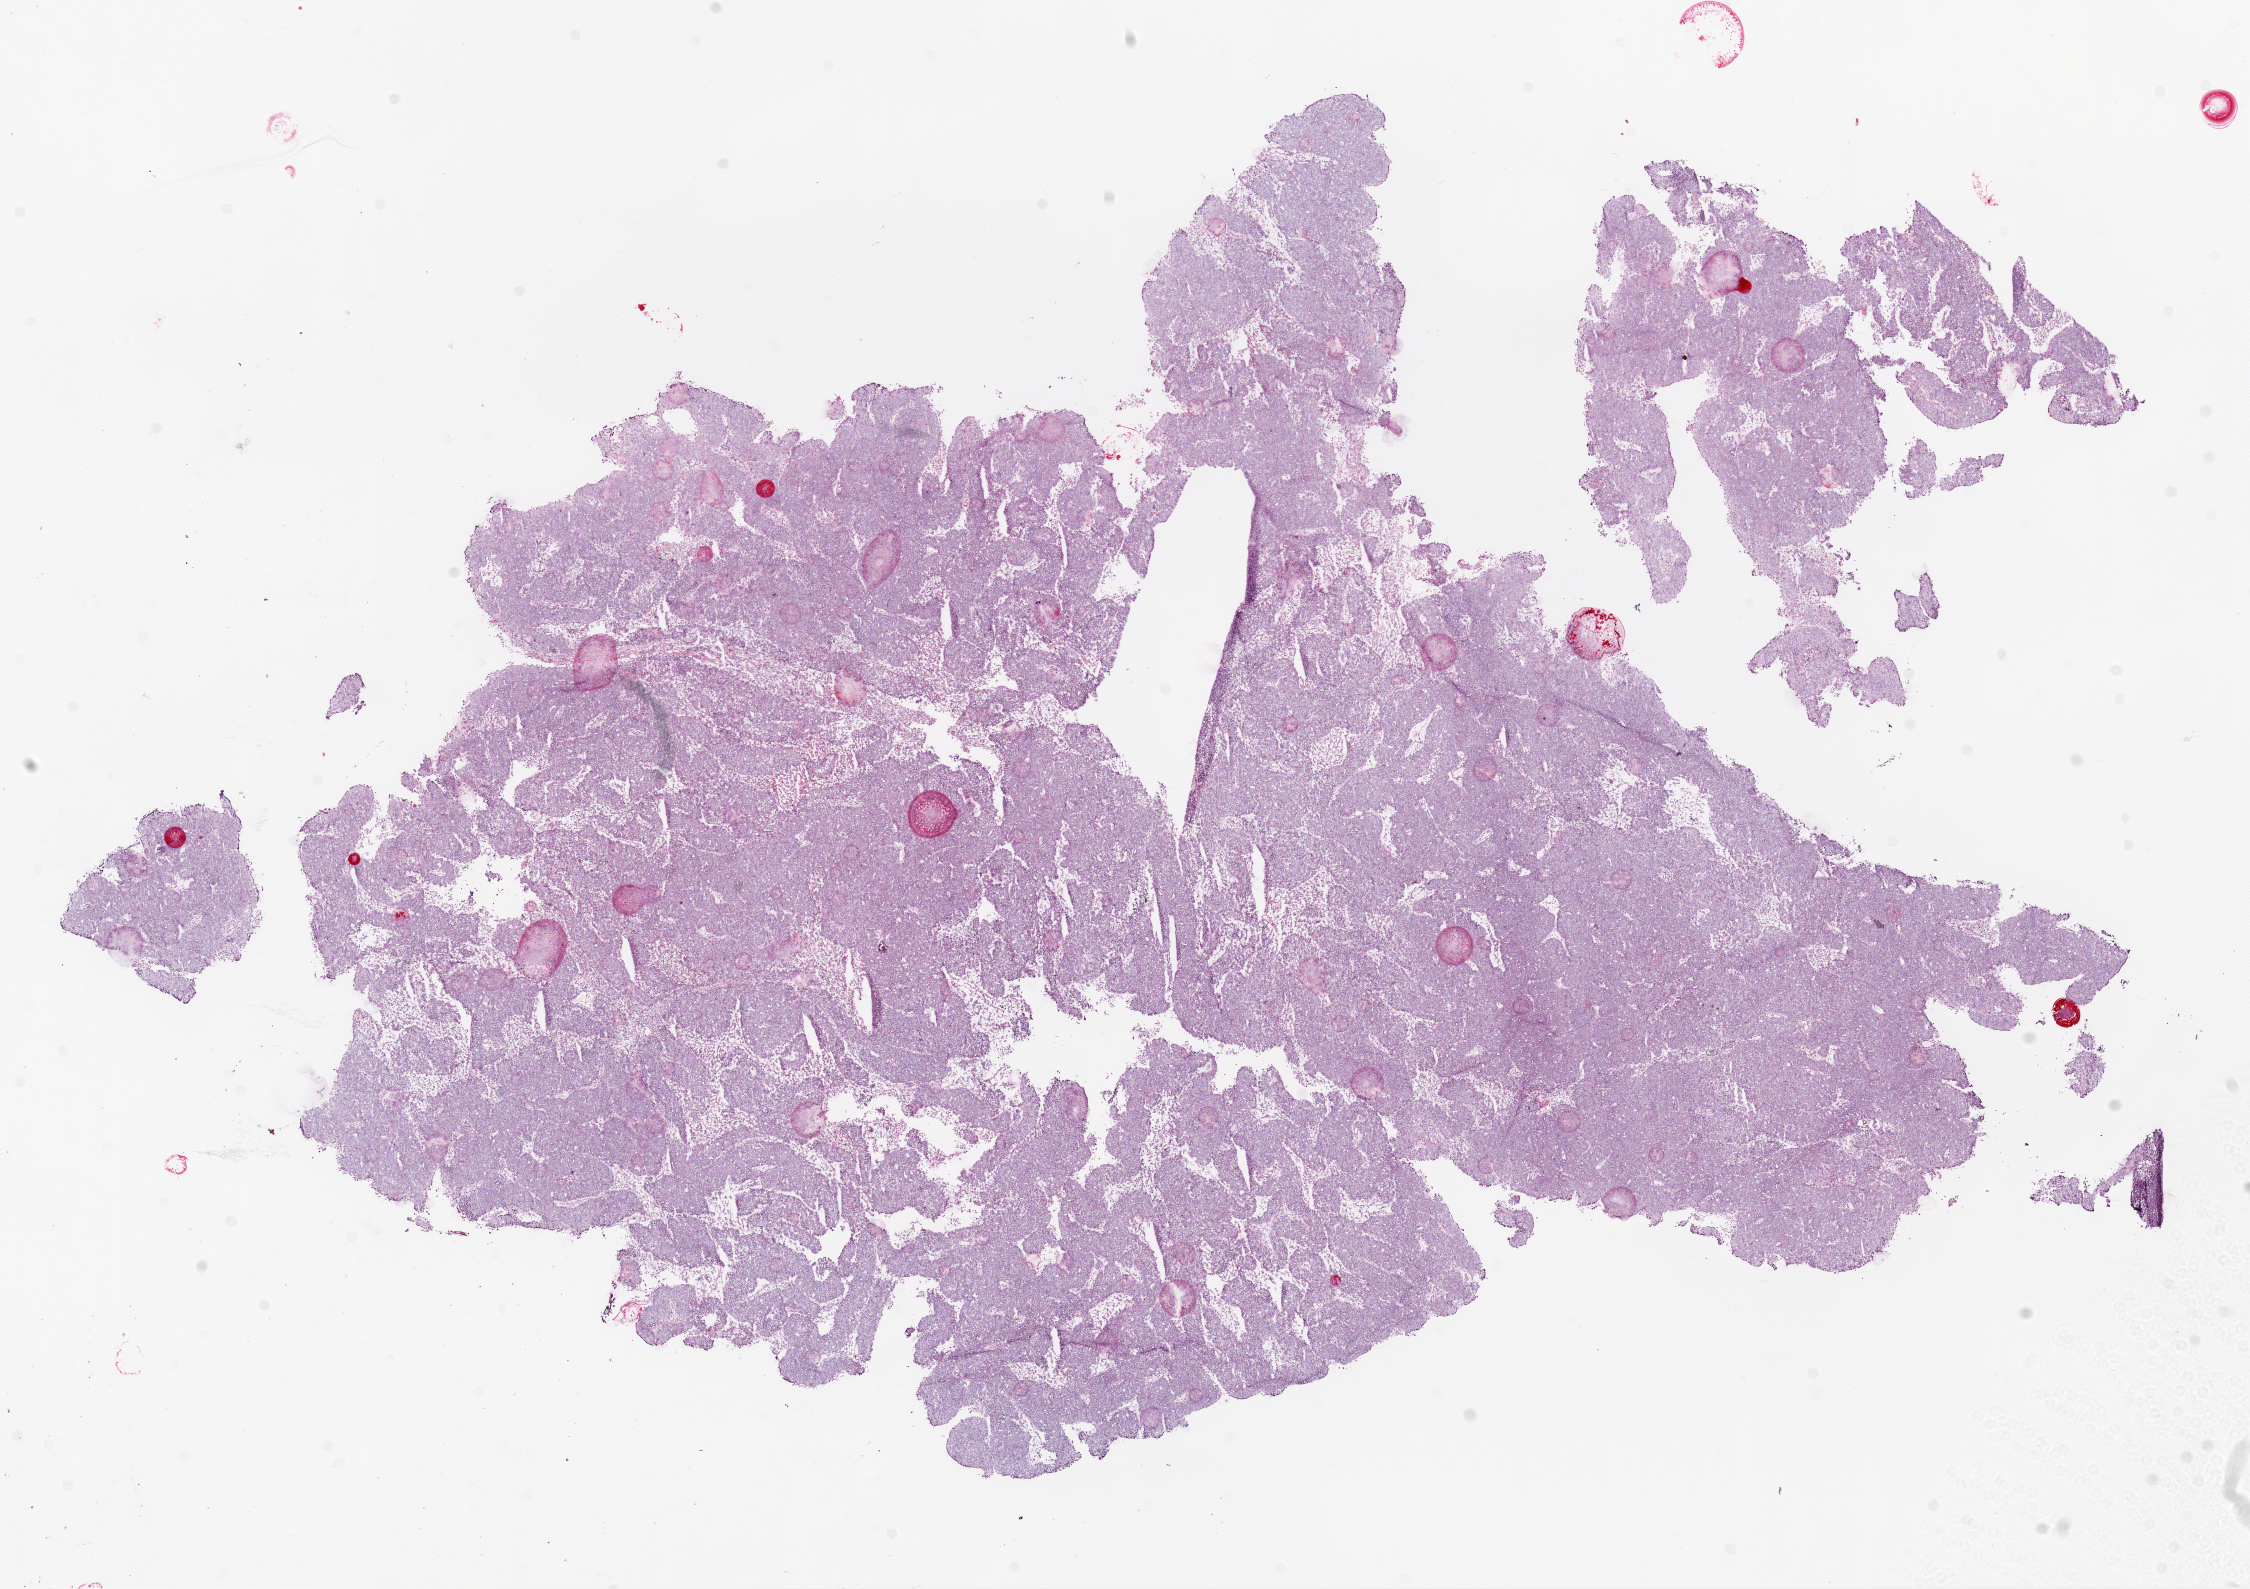
Digitized H&E-stained tissue section (whole slide) — shown as a low-resolution overview of the whole scanned area (about 18.1 x 12.8 mm). Frozen section. Sample: recurrent tumour, ovary. Female patient; age at initial diagnosis 41 years. Composition of this section per pathologist review: tumour cells 90%, tumour nuclei 95%, normal cells 0%, stromal cells 10%, necrosis 0%.
This section: recurrent tumour. Patient diagnosis: Serous cystadenocarcinoma, NOS.